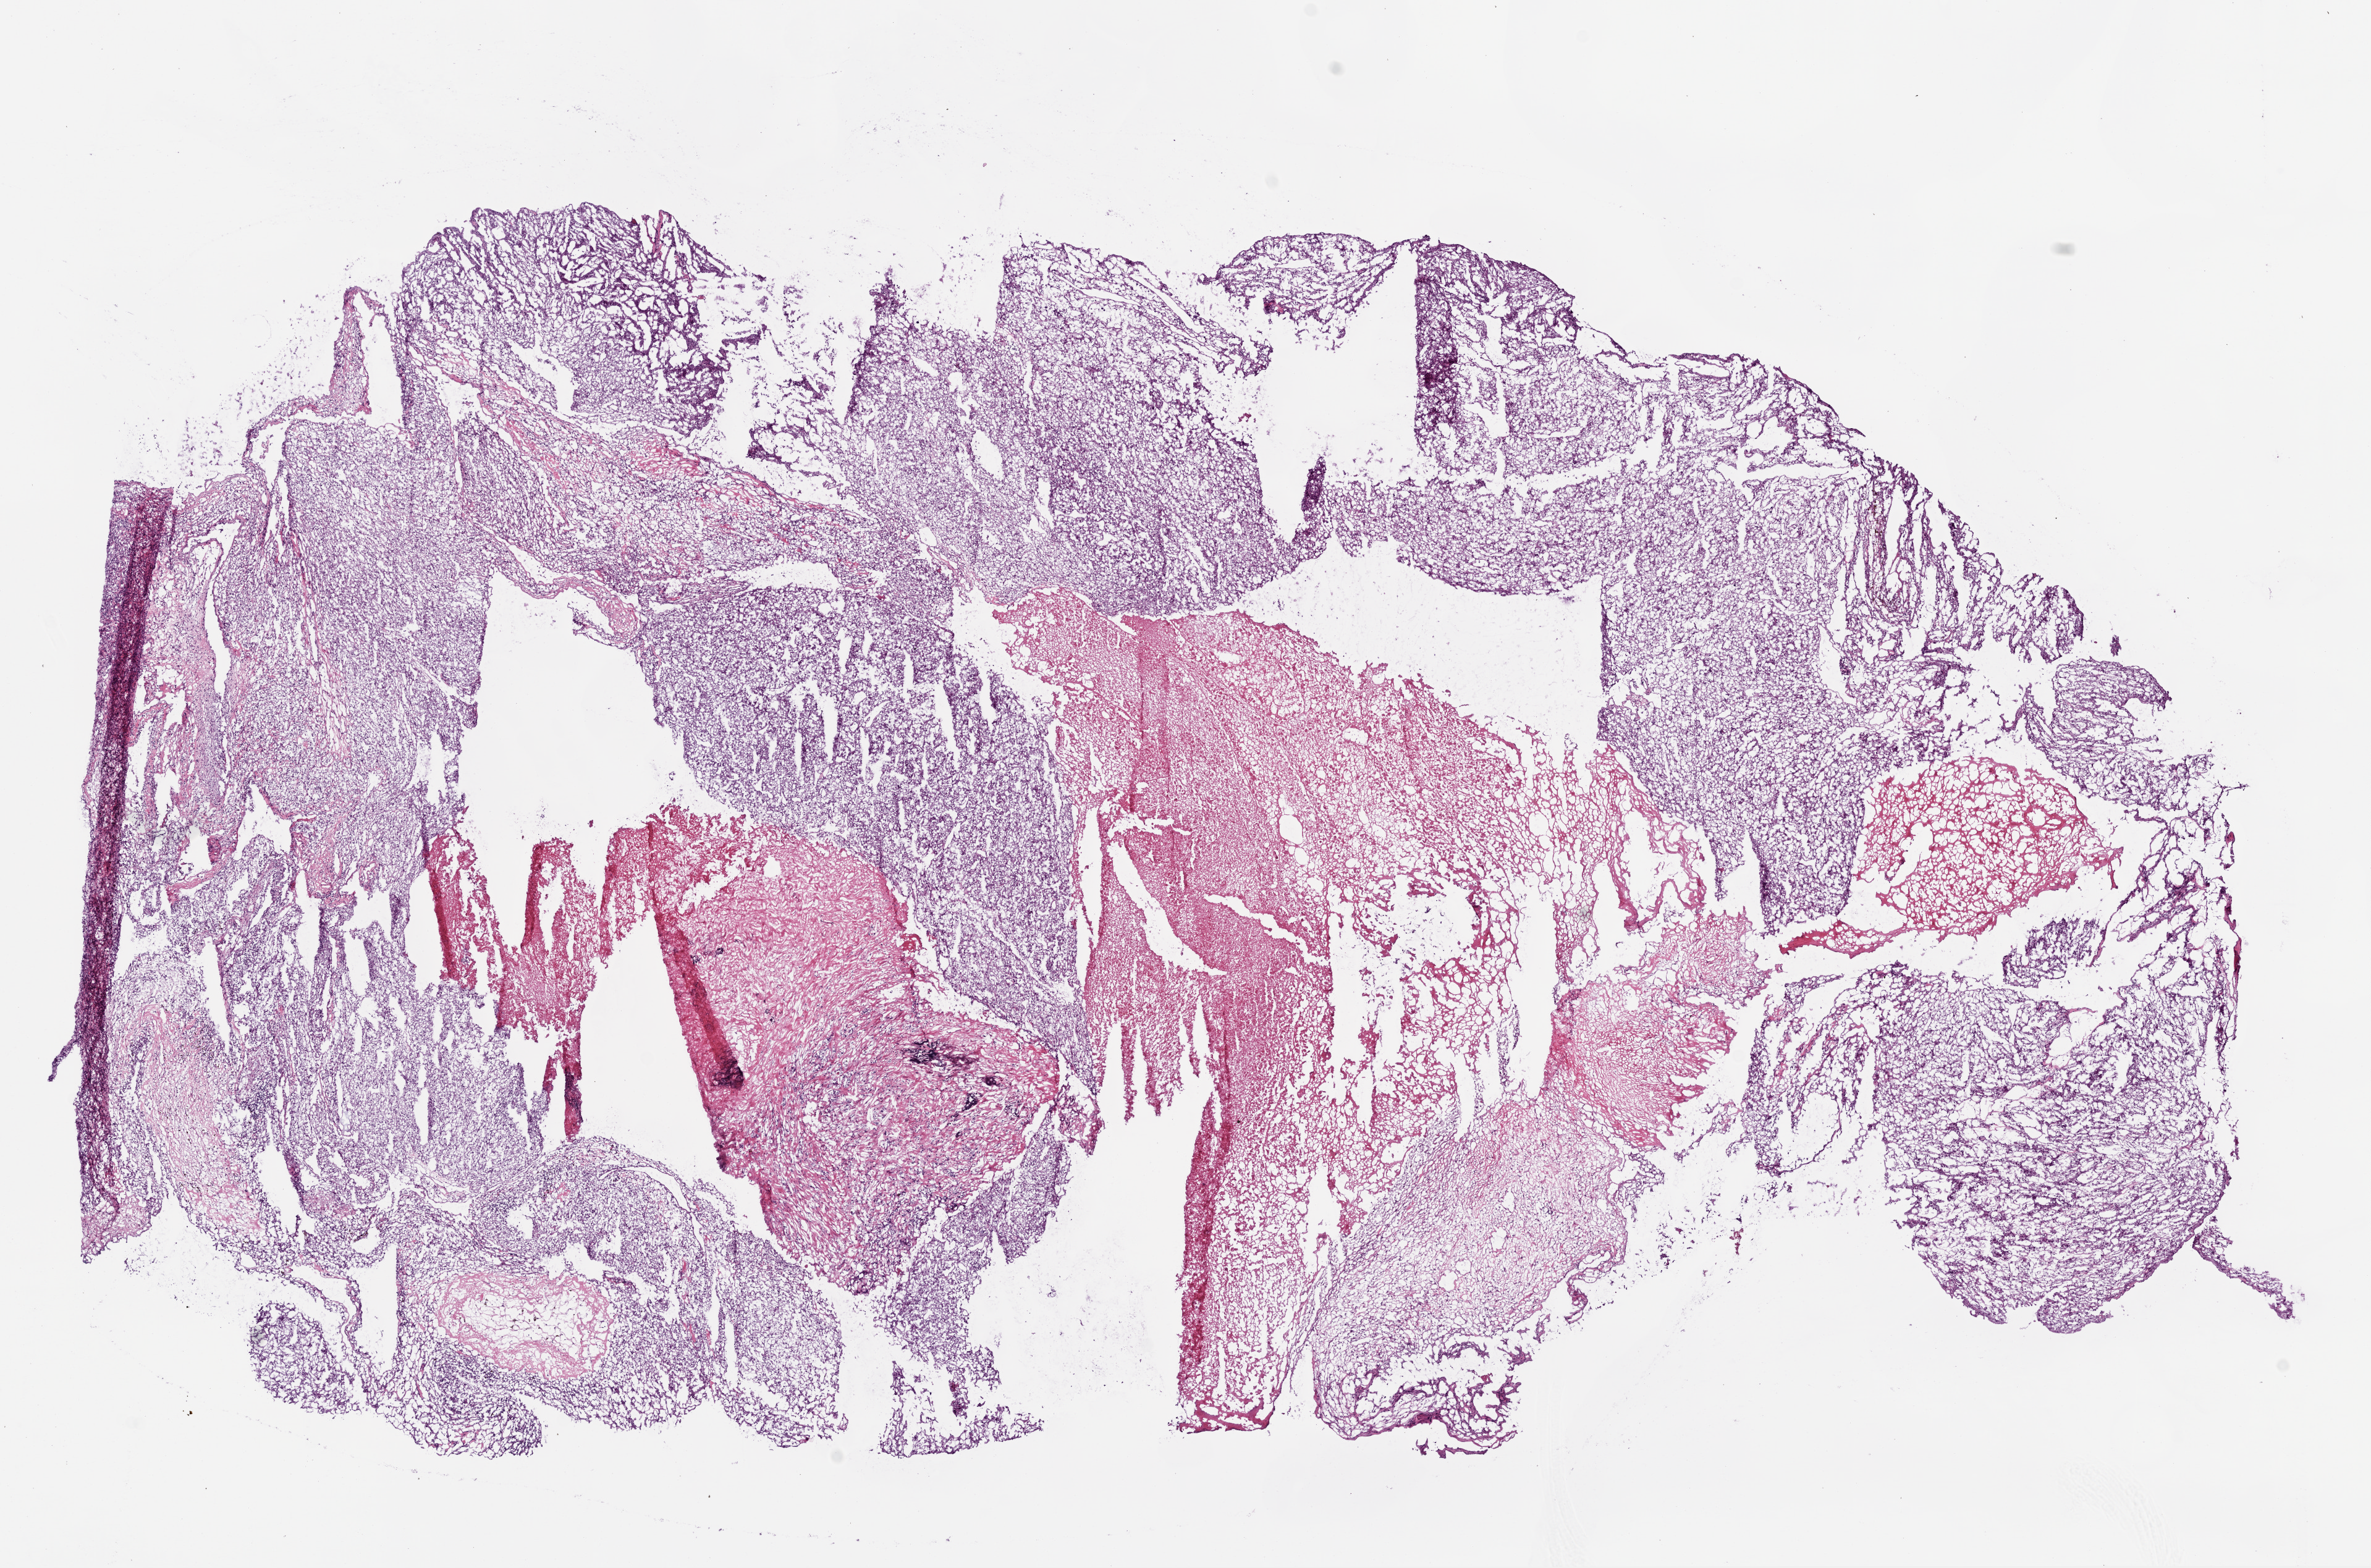
Whole-slide histology image, H&E-stained — whole scanned area (about 15.5 x 10.2 mm, acquisition: 20x scan) shown as a low-resolution overview. Frozen section. Sample: primary tumour, kidney. Female, age 59 years at initial diagnosis. Histologic grade: G3 (poorly differentiated). Composition of this section per pathologist review: tumour cells 70%, tumour nuclei 85%, normal cells 0%, stromal cells 10%, necrosis 20%.
AJCC pathologic stage: I. Diagnosis: Clear cell adenocarcinoma, NOS.